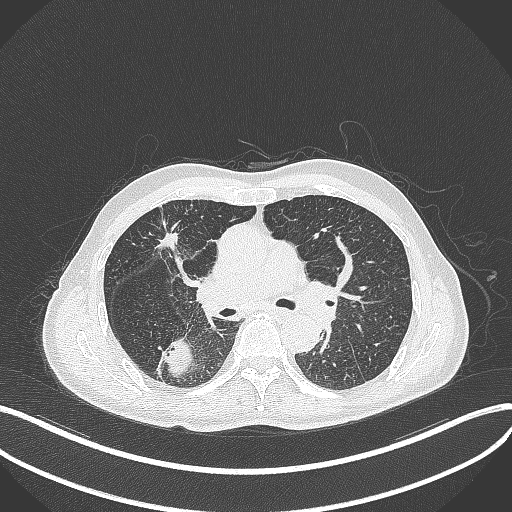
Chest CT, one axial slice; slice 270 of 428 in the series (ordered by position); 120 kVp; lung window (W 1500 / L -600 HU); 512 × 512 image matrix, field of view 400 × 400 mm. Male patient, age 79 years. Case-level facts recorded for this patient, not image findings: clinical TNM (as recorded): T3 N0 M0.
Outlined on this slice (bounding box drawn by a radiologist):
- lung tumour (recorded histology: adenocarcinoma): bounding box (x1, y1, x2, y2) in pixels: (160, 339, 194, 379)